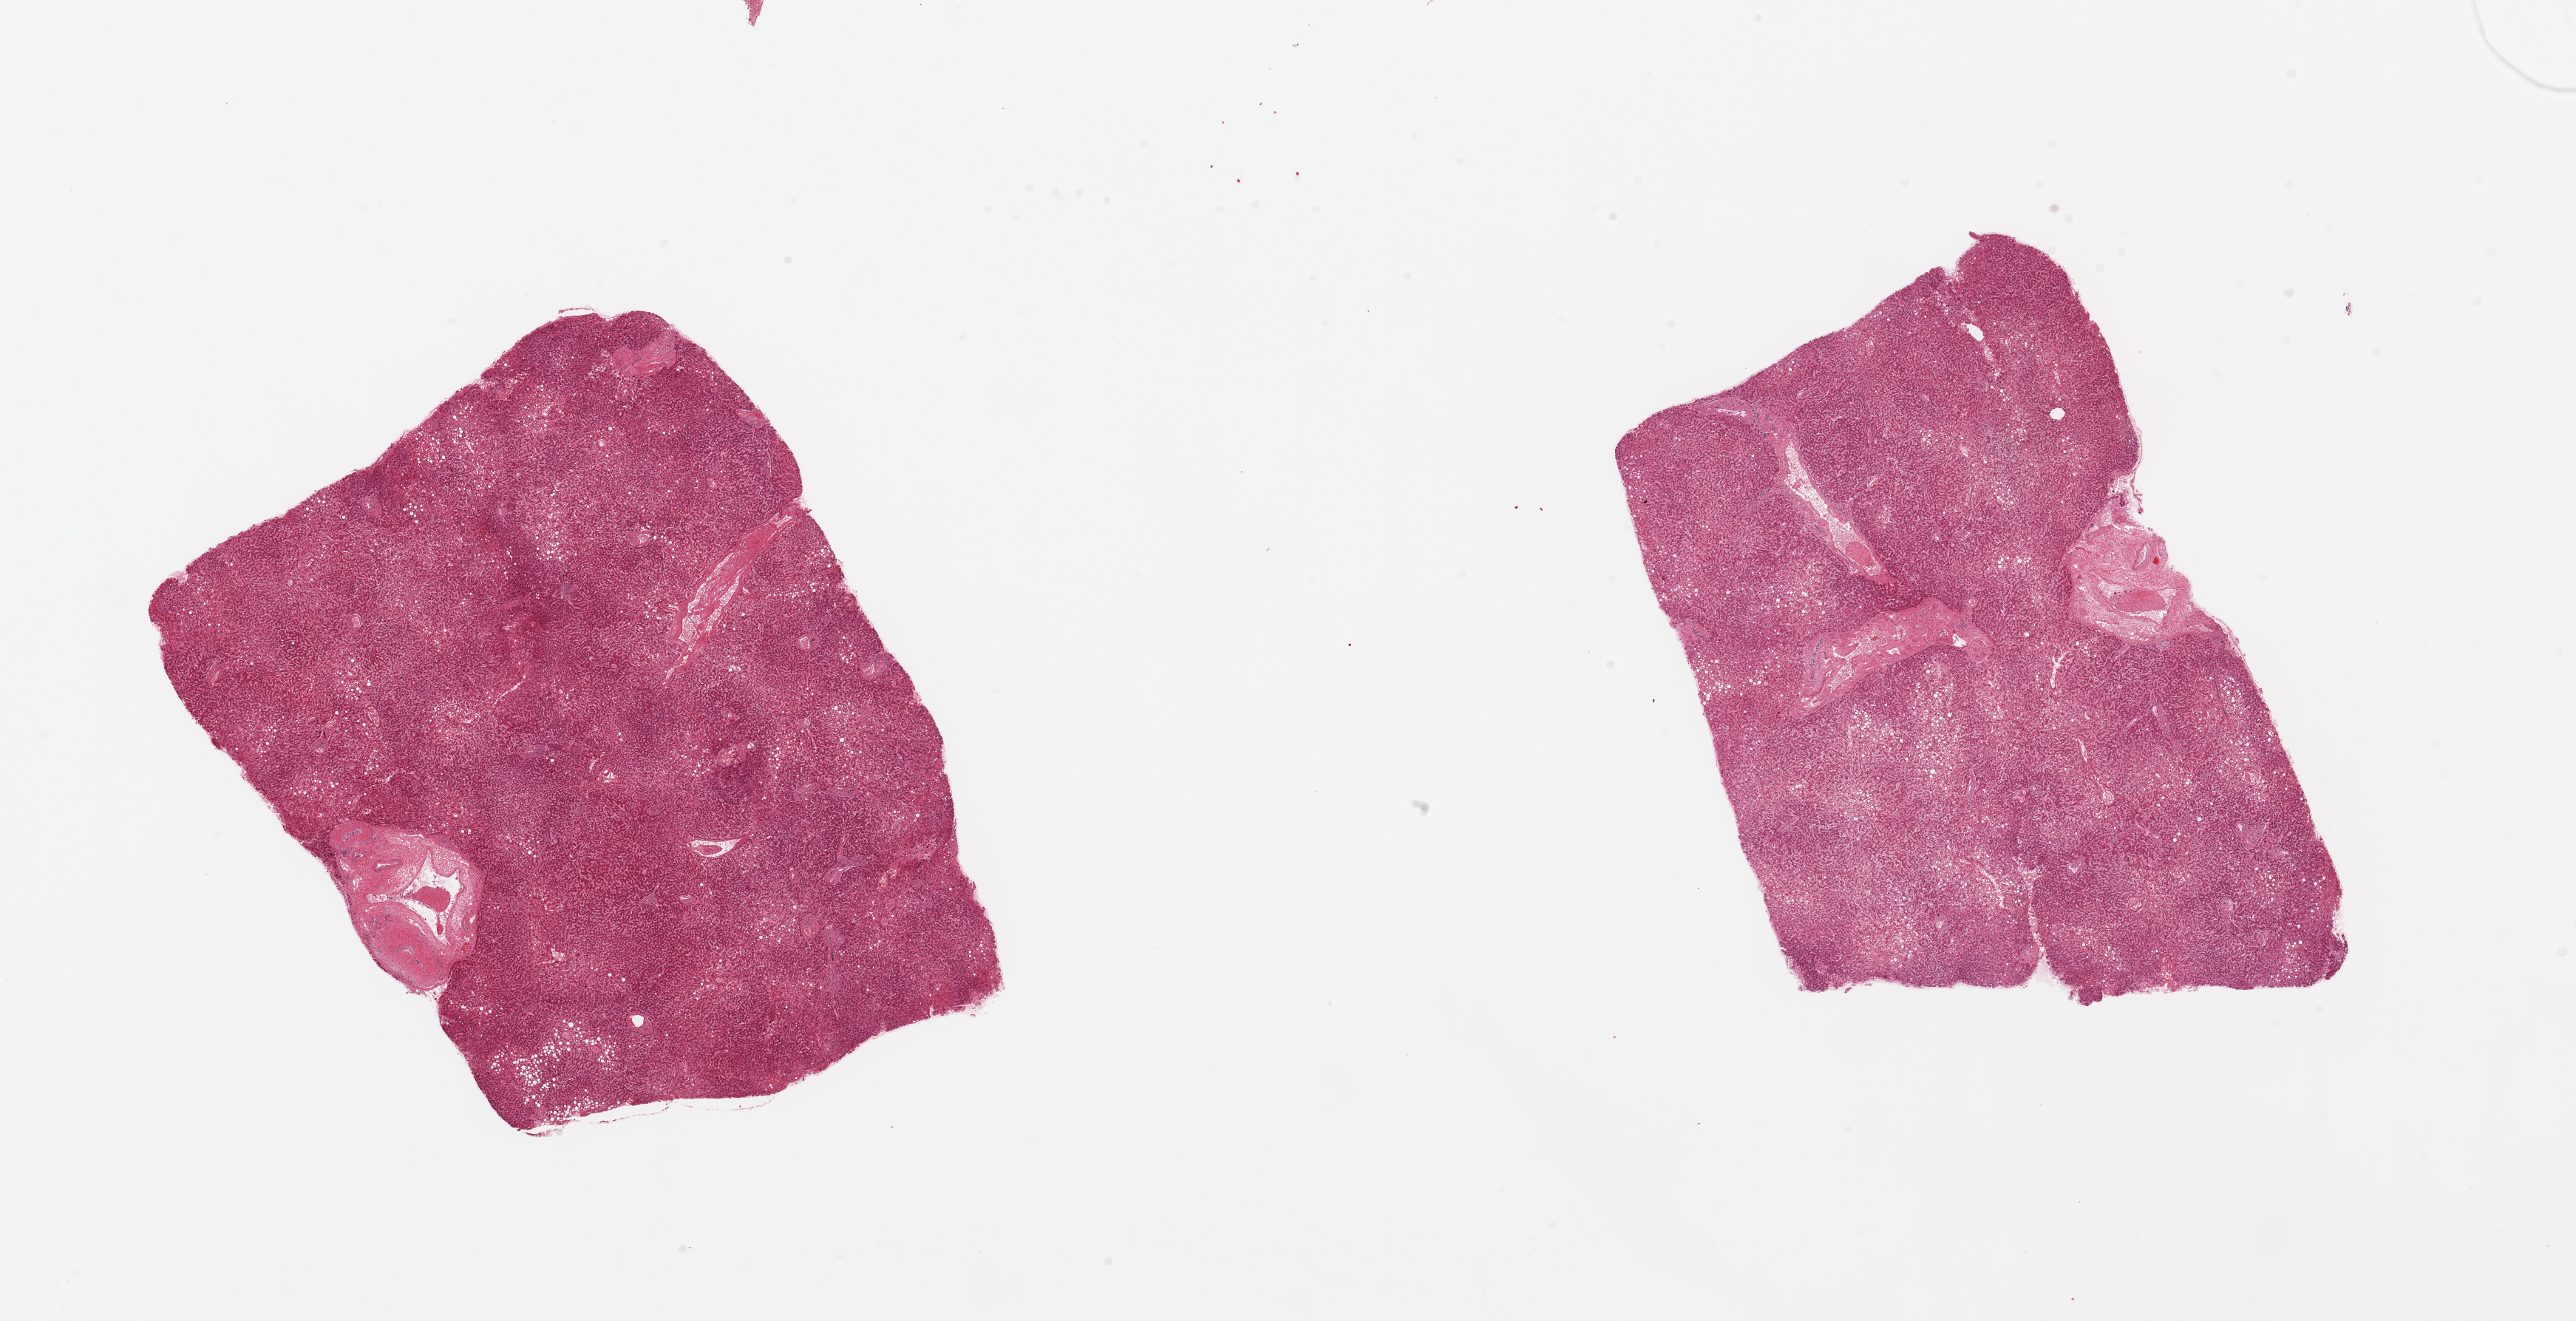
Hematoxylin and eosin (H&E) whole-slide image, shown as a low-resolution overview of the whole scanned area (about 27.6 x 14.1 mm, slide scanned at 20x), PAXgene-fixed paraffin-embedded (PFPE) section, sampled site (target tissue): liver, tissue donor sample. Donor: female.
Pathologist's review note for this sample: 2 pieces; moderate macrovesicular steatosis.